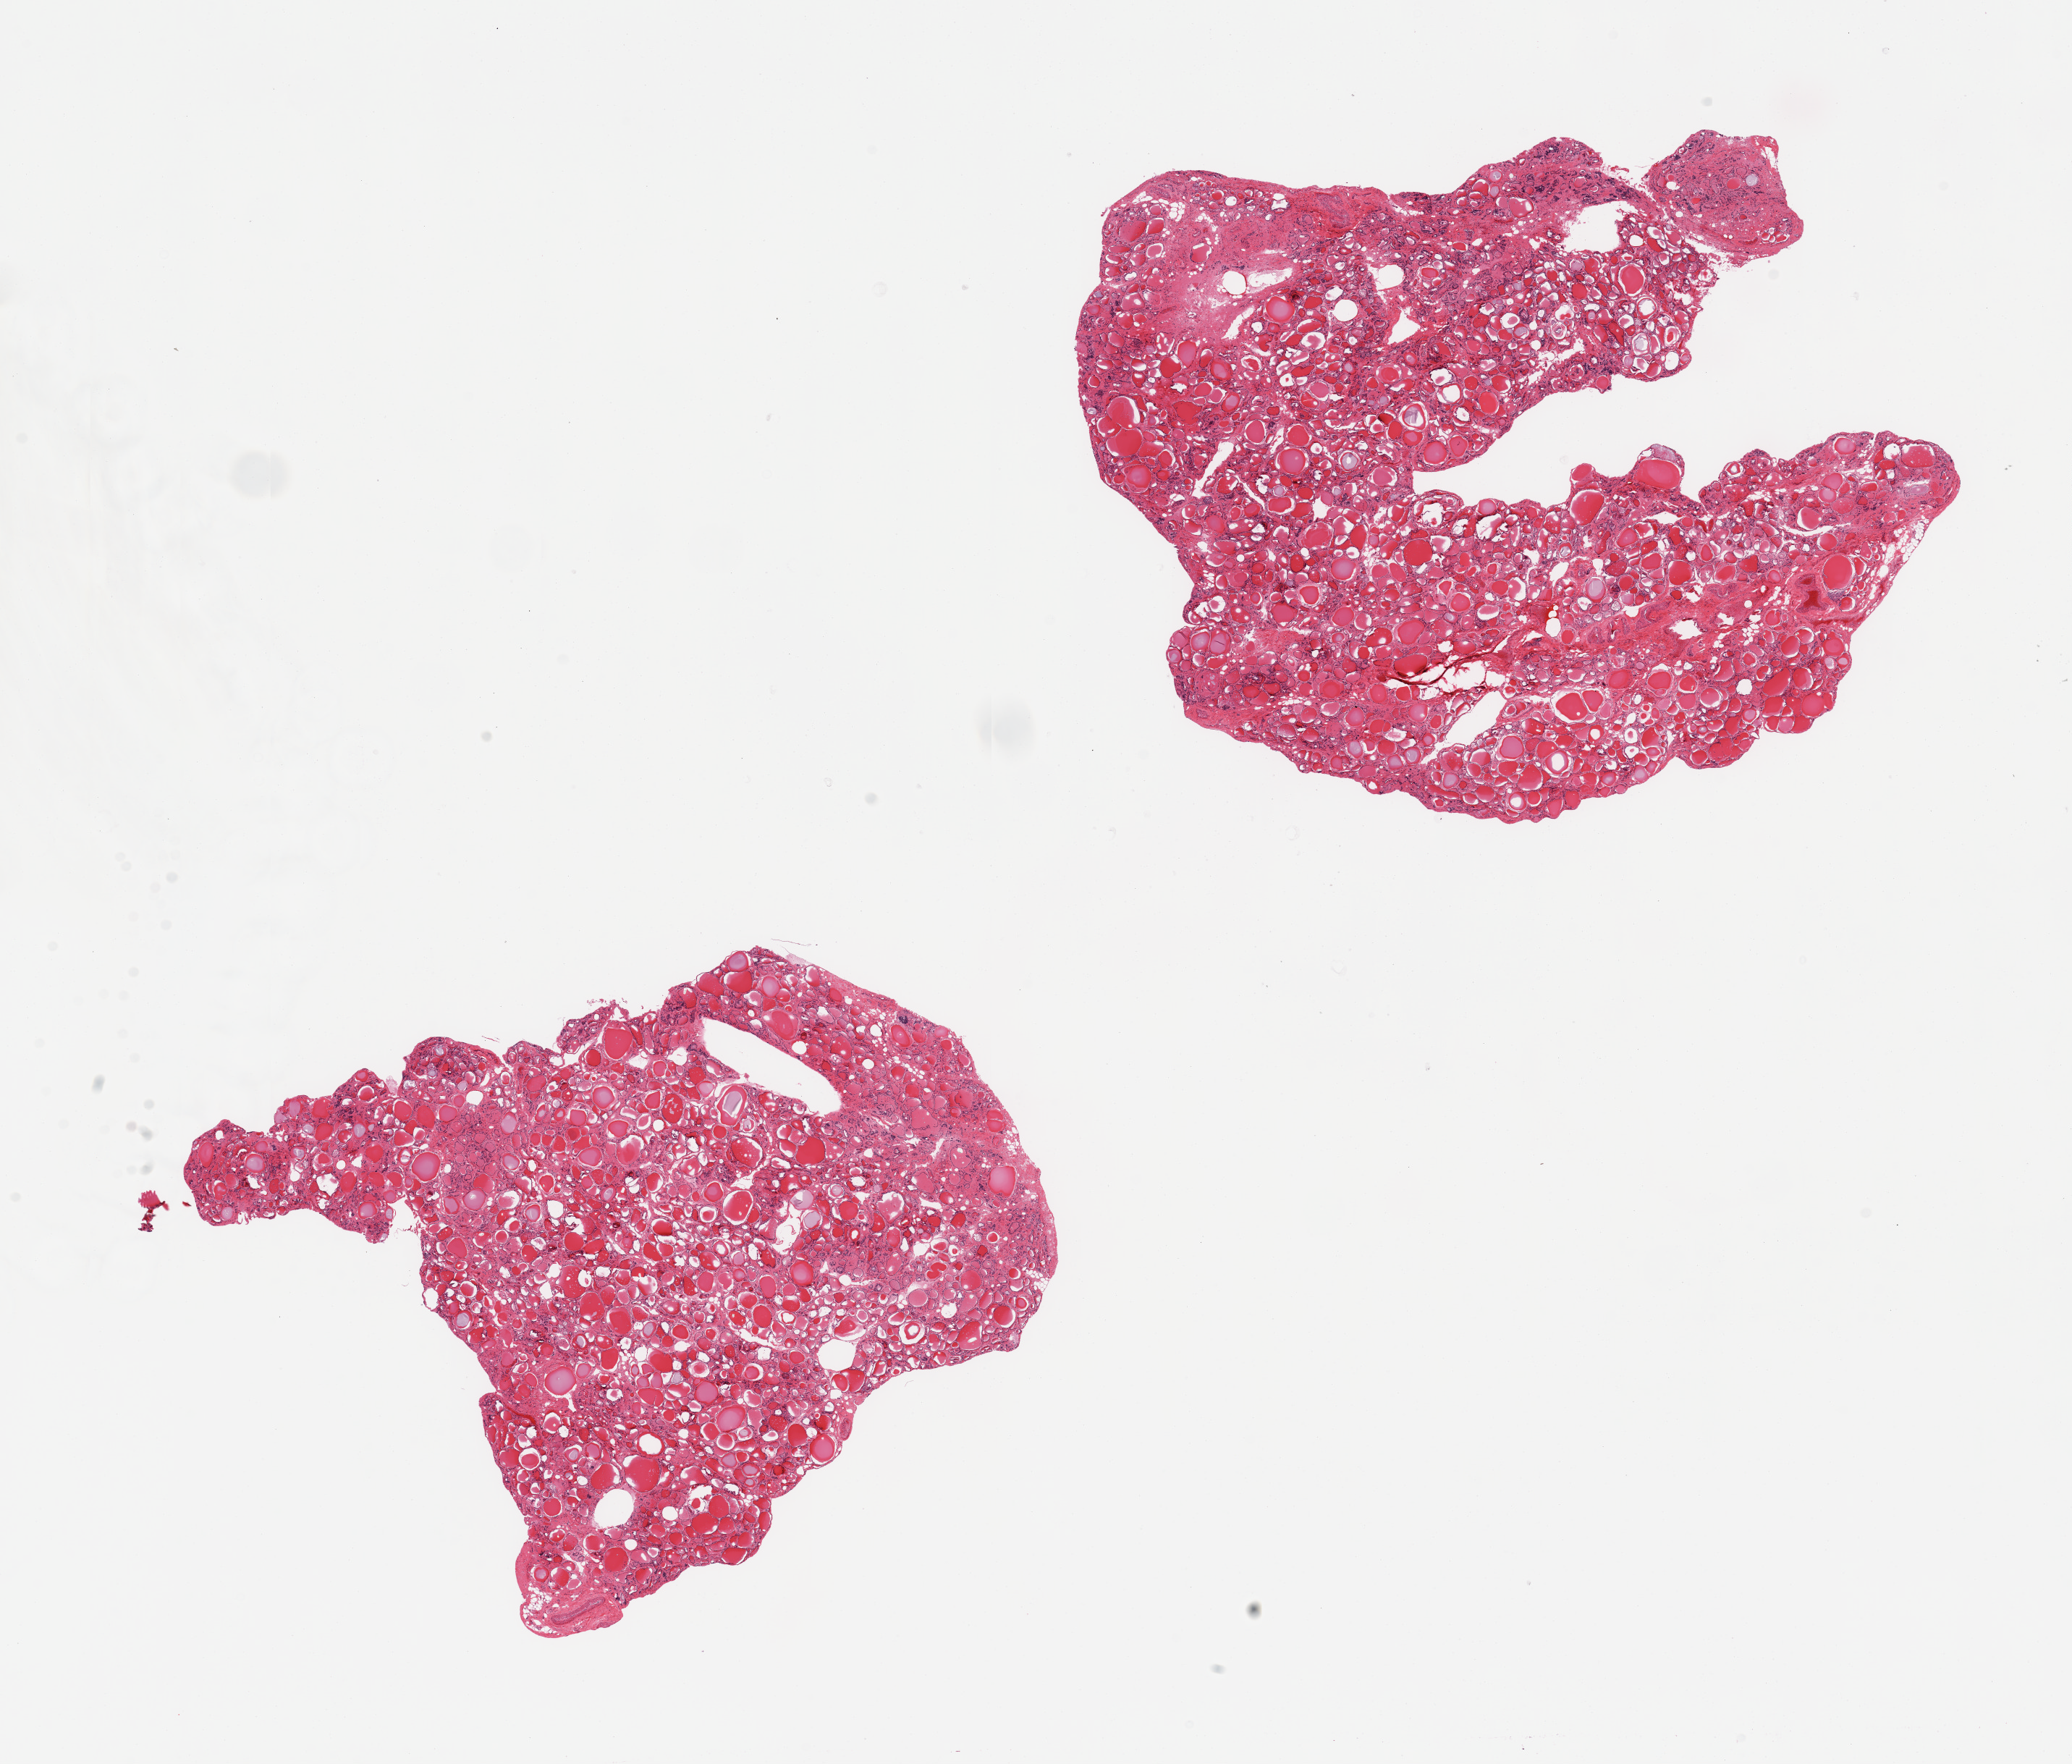
Digitized H&E-stained section — low-resolution overview of the scanned area, about 22.6 x 19.3 mm. PAXgene-fixed paraffin-embedded (PFPE) section. Sampled site (target tissue): thyroid. Donor tissue sample.
• pathologist's review note for this sample: 2 pieces, moderately autolyzed but no abnormalities